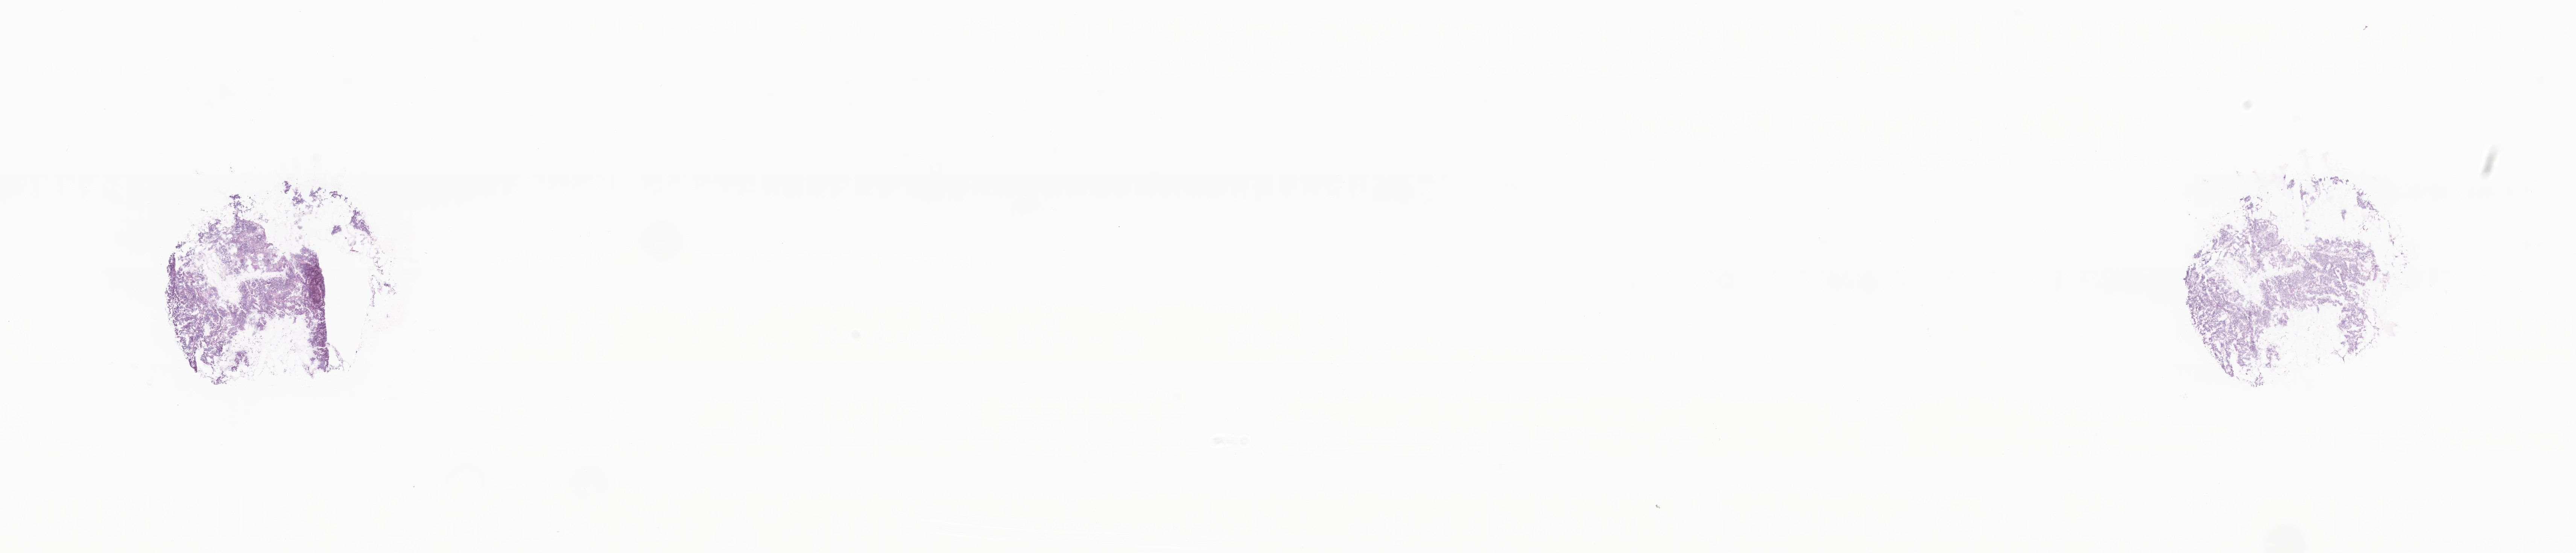
Hematoxylin and eosin (H&E) whole-slide image — a low-resolution overview of the entire scanned area, about 28.9 x 6.2 mm. Frozen section. Primary tumor. Site: ascending colon. Patient: female. Composition of this section per pathologist review: tumor cells 84%, tumor nuclei 95%, stromal cells 15%, necrosis 1%, normal cells 0%. Infiltration values recorded for this section: lymphocyte infiltration 2%, monocyte infiltration 1%, neutrophil infiltration 0%.
Section: top of the tissue portion. Histologic diagnosis: Adenocarcinoma, NOS.